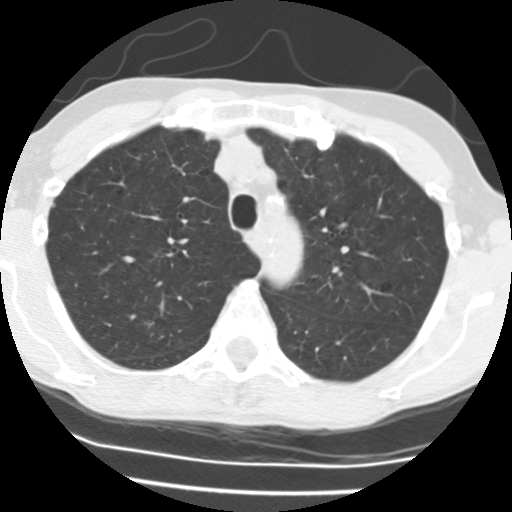
Low-dose screening chest CT, axial slice. Third annual screen. Lung window (W 1500 / L -600 HU). 2.5 mm slice thickness. 120 kVp. Female participant, aged 58 years at enrolment.
Expert reader's lesion annotation, bounding box [x1, y1, x2, y2] px = [130, 313, 172, 355]. The screening reader recorded 3 non-calcified nodules or masses ≥4 mm on this exam (right upper lobe, left upper lobe, right upper lobe); which of them this box marks is not recorded. Later outcome: lung cancer diagnosed 153 days after this screen — bronchiolo-alveolar adenocarcinoma, NOS, right upper lobe, well differentiated (G1), stage IA (AJCC 6th edition), 8 mm at pathology.